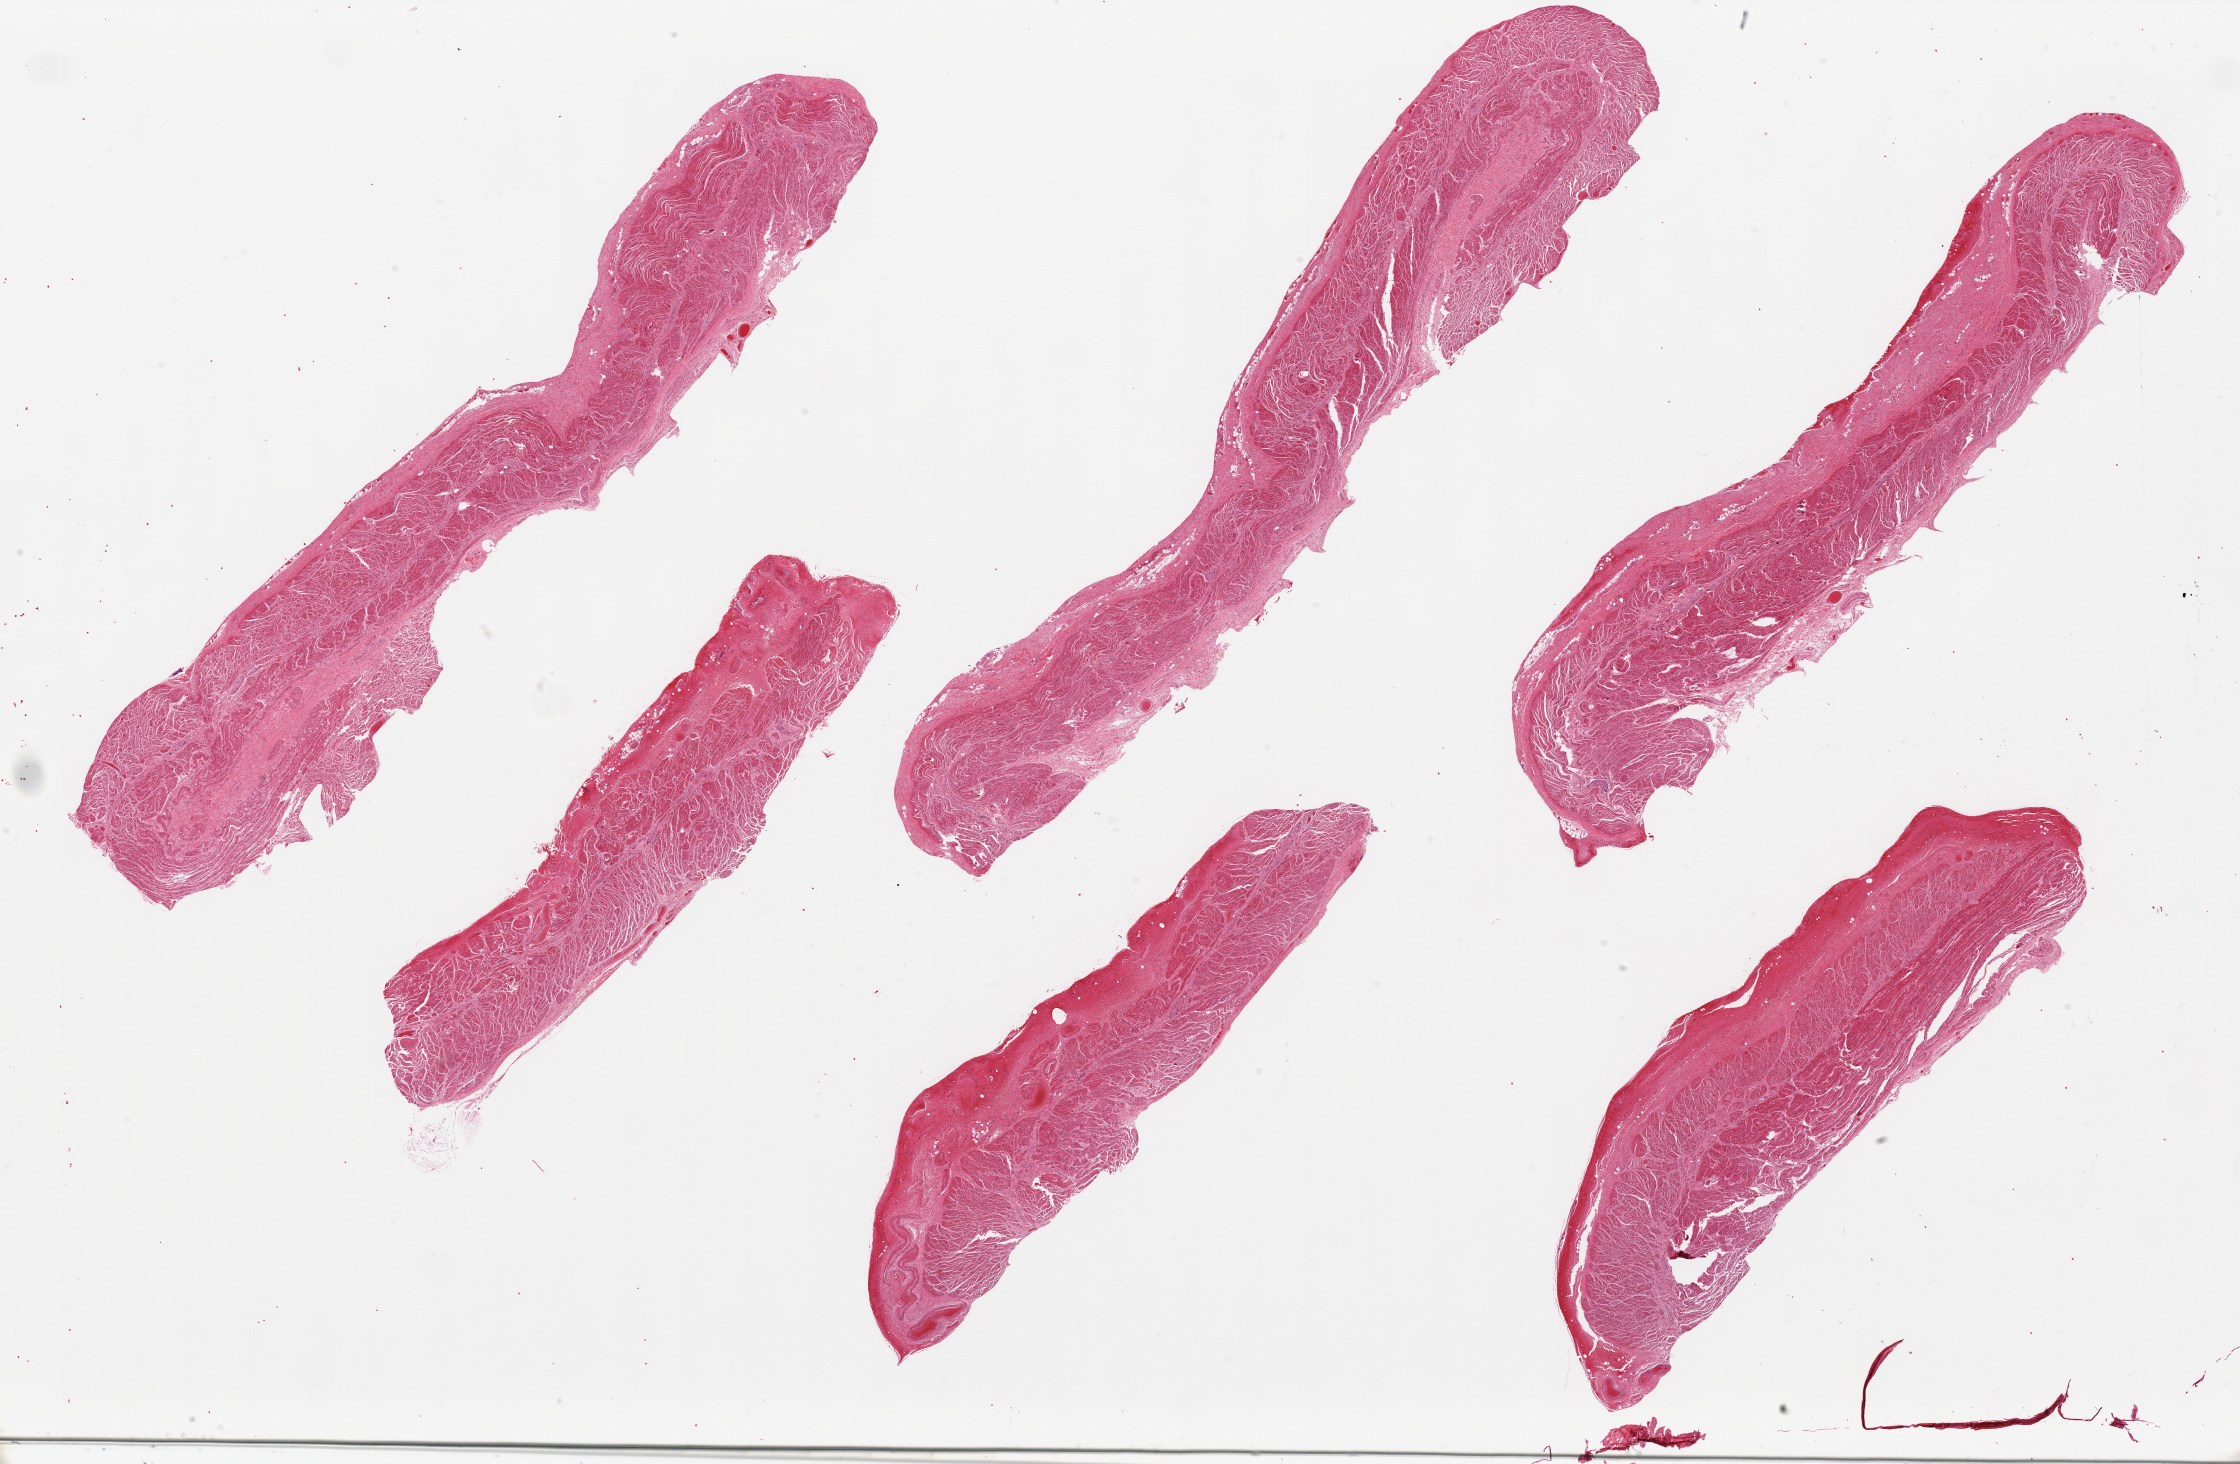
Digitized H&E-stained section, whole scanned area (about 35.4 x 23.2 mm, slide scanned at 20x) shown as a low-resolution overview. PAXgene-fixed, paraffin-embedded tissue. Target tissue: gastroesophageal junction. Donor tissue sample. Donor sex: female.
Review note (as recorded): 6 pieces, all muscualris, good specimens.